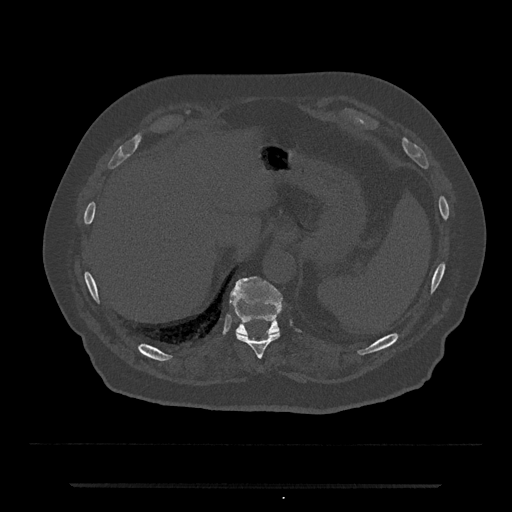
CT including the spine, one axial slice; slice 684 of 797 in the series (ordered by position); 120 kVp; bone window (W 1800 / L 400 HU); 0.5 mm slice thickness; 512 × 512 image matrix, field of view 434 × 434 mm. Male patient, age 80 years. Case-level facts recorded for this patient, not image findings: primary cancer: prostate.
Outlined on this slice (semi-automatic segmentation, software-assisted and operator-edited):
- T10 vertebra: bounding box (x1, y1, x2, y2) in pixels: (236, 331, 280, 359)
- T11 vertebra: (230, 276, 283, 335)